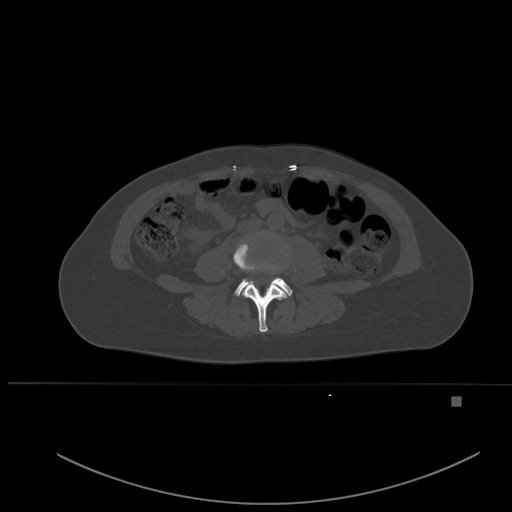
CT including the spine, one axial slice. Slice 184 of 651 in the series (ordered by position). Bone window (W 1800 / L 400 HU). 1.5 mm slice thickness. 512 × 512 image matrix, field of view 443 × 443 mm. Female patient, age 49 years. From the clinical record (not read from this slice): primary cancer: breast; vertebrae with lytic lesions (as recorded): L3, T12, L4.
Annotated regions visible in this slice (semi-automatic segmentation, software-assisted and operator-edited):
- L3 vertebra: bounding box <233,243,287,333> (left, top, right, bottom; pixels)
- L4 vertebra: <235,258,292,296>